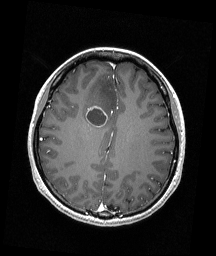
Brain MRI from a brain-tumour surgery series, one axial slice; slice 70 of 192 in the series (ordered by position); T1-weighted post-contrast; 1 mm slice thickness; 216 × 256 image matrix, field of view 211 × 250 mm. From the clinical record (not read from this slice): histopathology: Astrocytoma; WHO grade: 4.
Outlined on this slice (manually delineated by an expert):
- tumour: bounding box (x1, y1, x2, y2) in pixels: (85, 106, 108, 127)